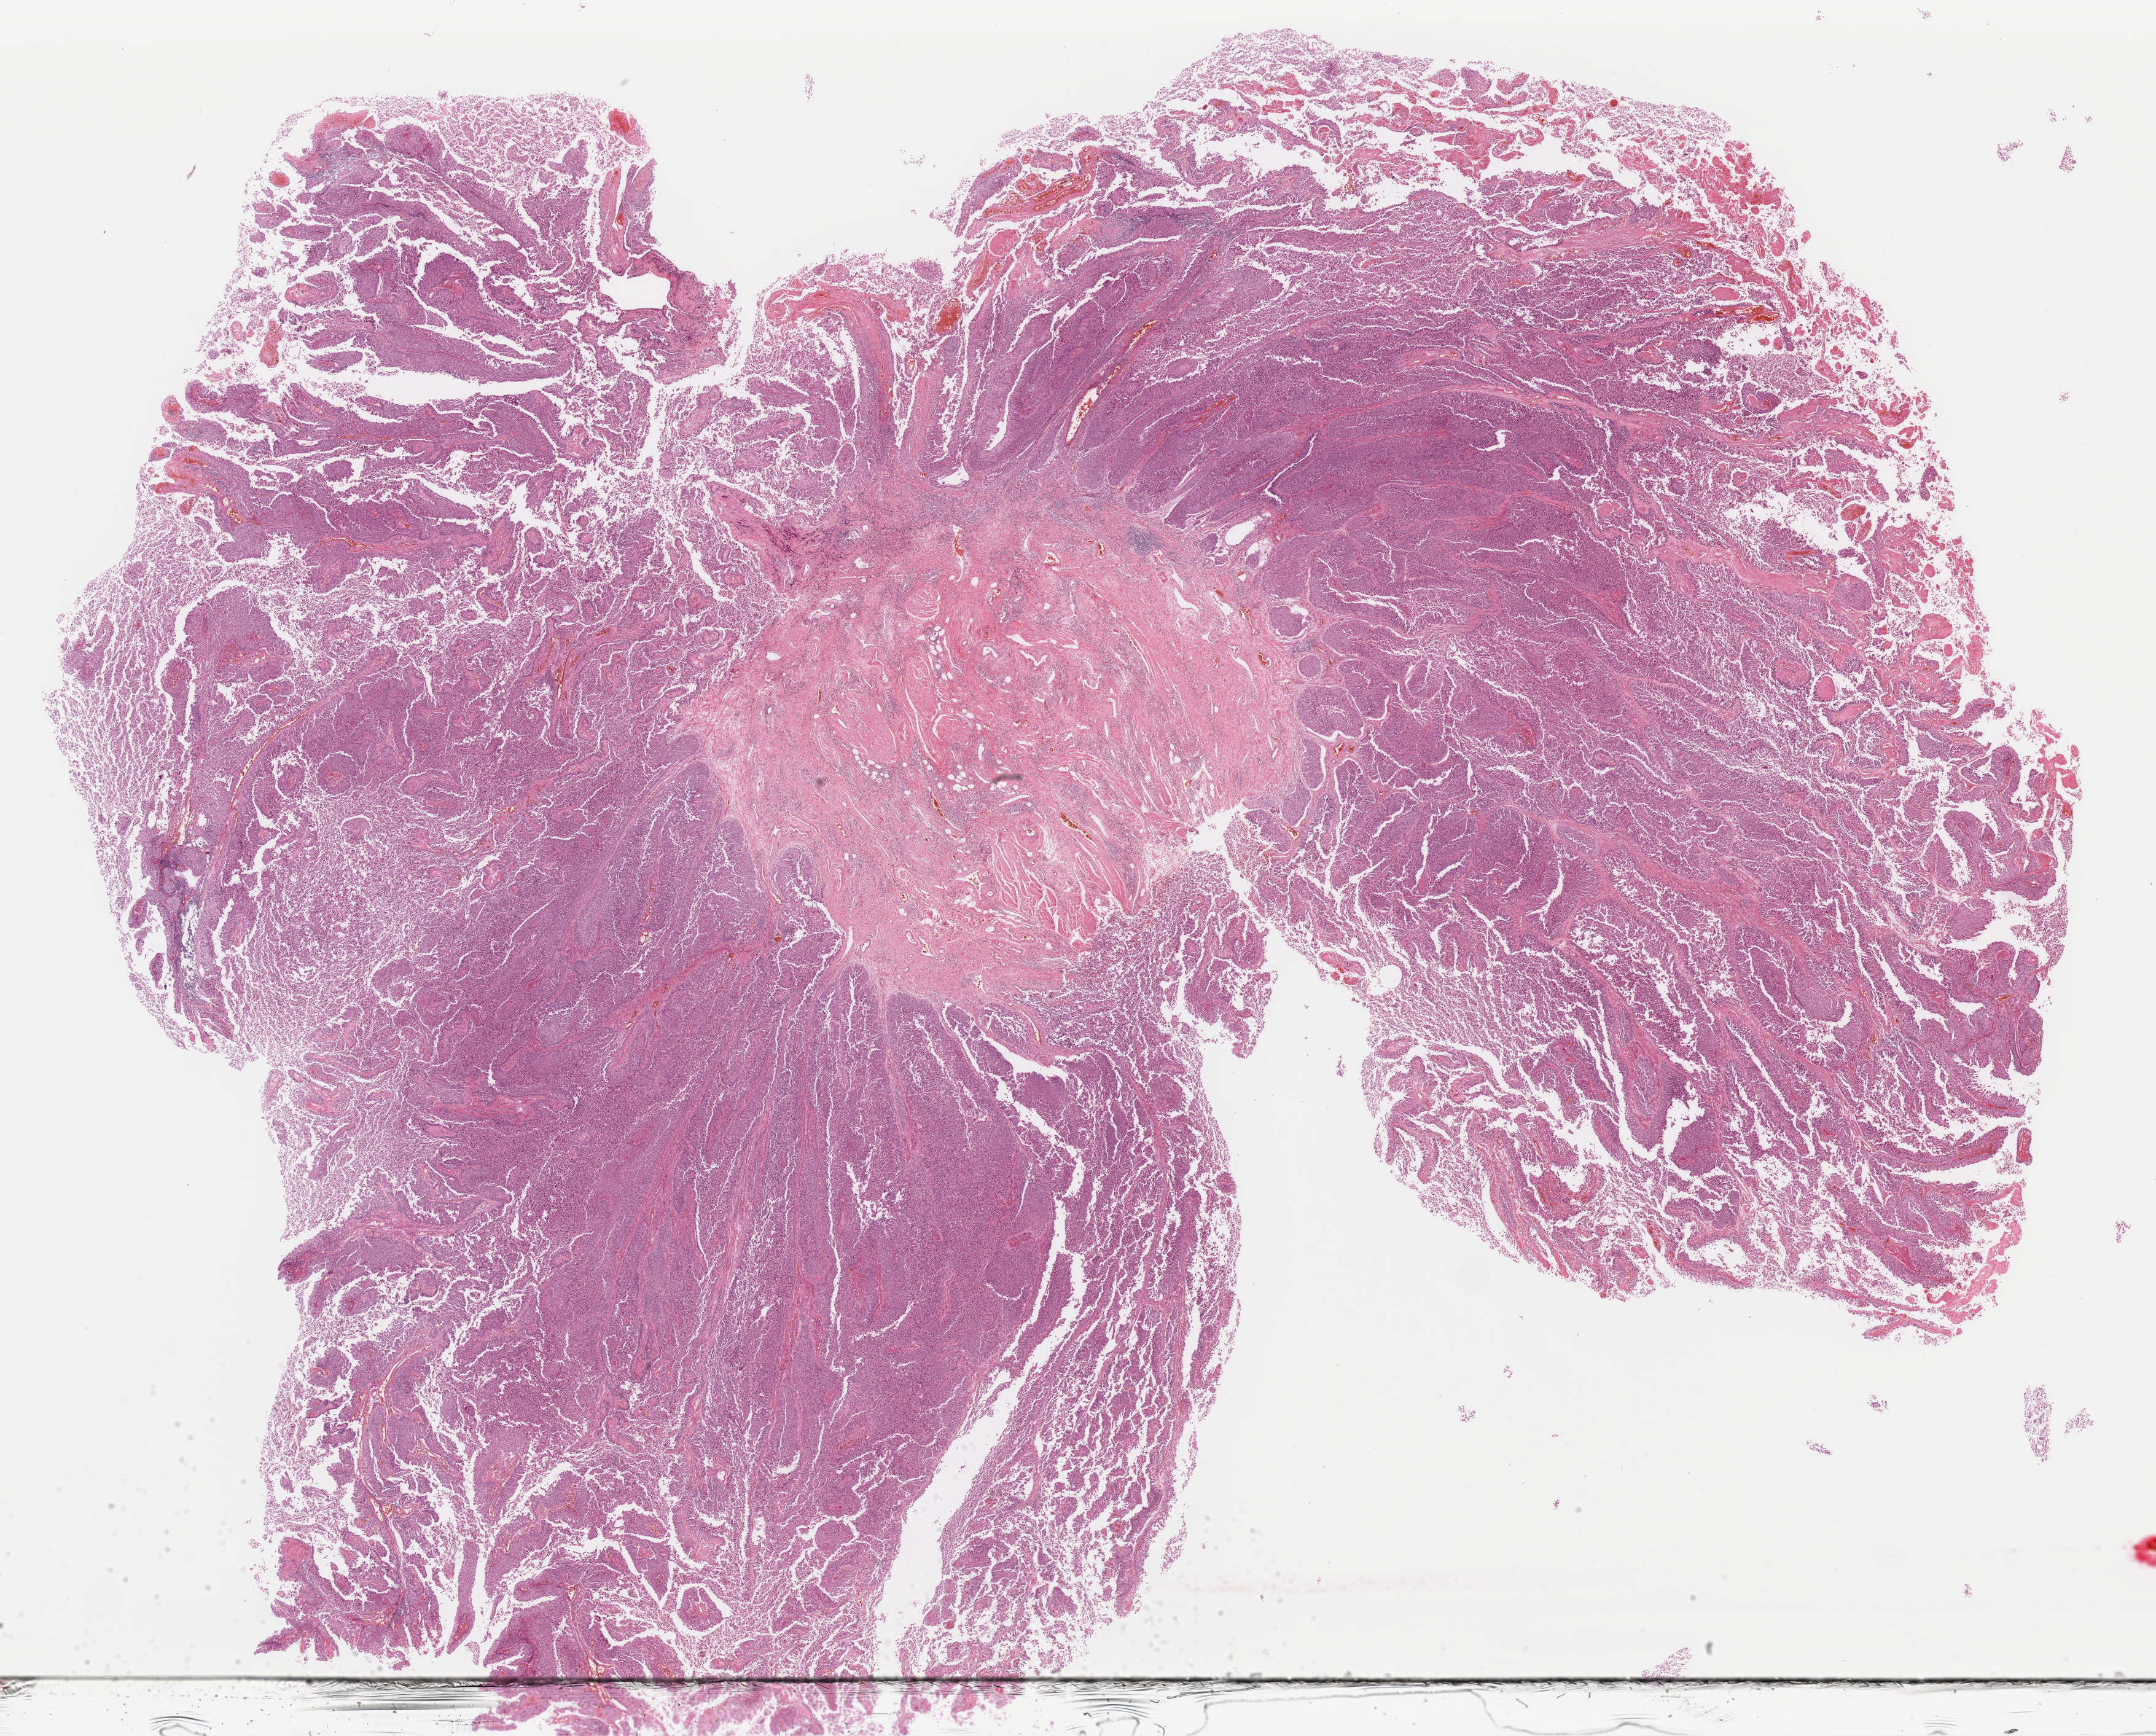
Hematoxylin and eosin (H&E) stained whole-slide image — shown as a low-resolution overview of the whole scanned area (about 27.7 x 22.3 mm, acquisition: 40x scan); formalin-fixed paraffin-embedded (FFPE) diagnostic section; sample: primary tumour, bladder. Patient: male, age at initial diagnosis 73 years. Histologic grade: low grade.
* pathologic diagnosis: Transitional cell carcinoma
* lymph nodes positive (case pathology): 0 of 14 examined
* AJCC pathologic stage: III (7th edition)